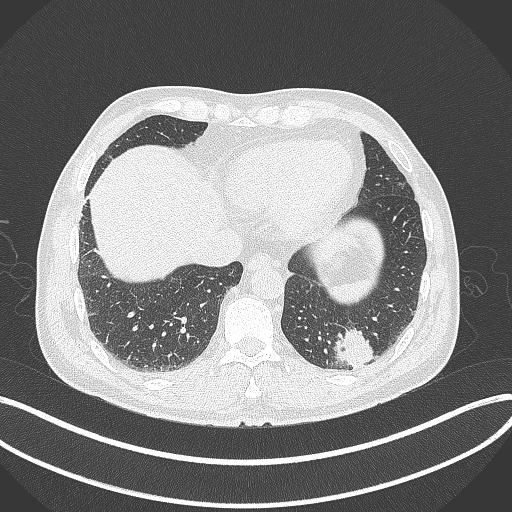
Chest CT, one axial slice; position 65 of 300 along the scan axis; reconstruction kernel B70f; 120 kVp; lung window (W 1500 / L -600 HU); 1 mm slice thickness; 512 × 512 image matrix, field of view 400 × 400 mm. Male patient, age 54 years. From the clinical record (not read from this slice): clinical TNM (as recorded): T1c N0 M1; histopathological grade: G3.
Annotated regions visible in this slice (rectangle marked by the reading radiologist):
- lung tumour (recorded histology: adenocarcinoma): bounding box (x1, y1, x2, y2) in pixels: (329, 323, 379, 371)